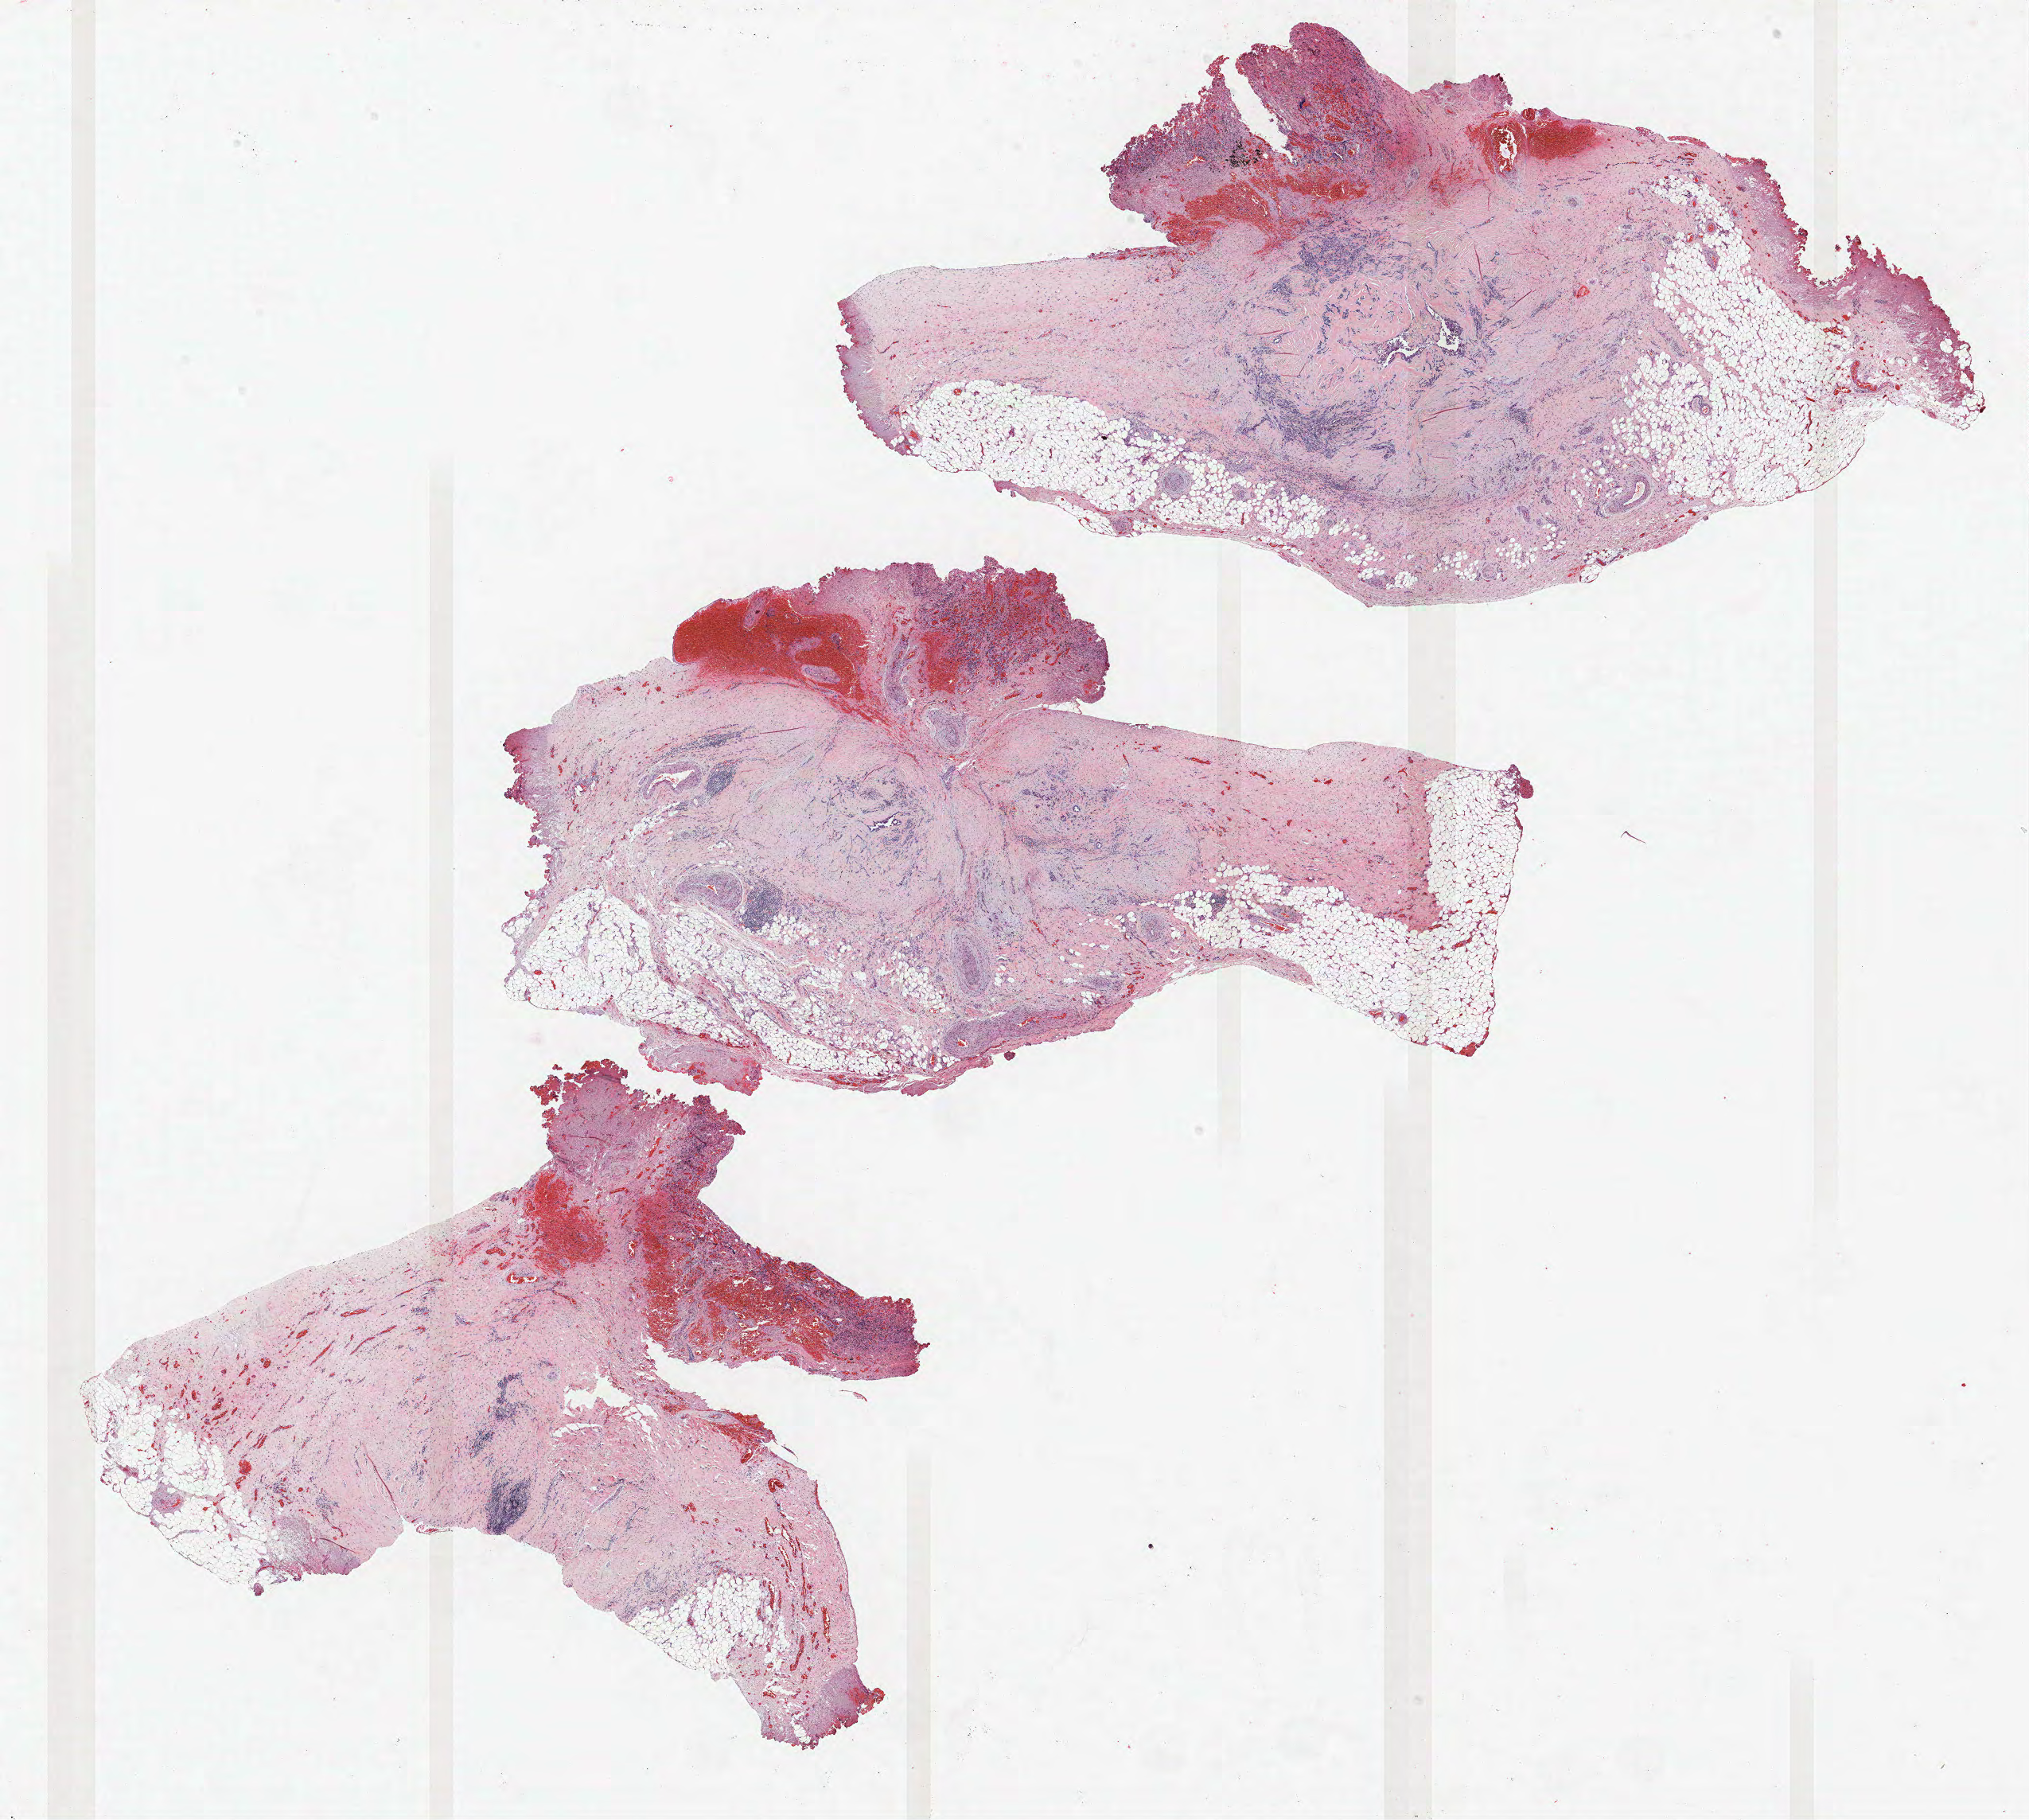
H&E-stained whole-slide image — low-resolution overview of the scanned area, about 20.4 x 18.3 mm (slide scanned at 40x); formalin-fixed paraffin-embedded (FFPE) section; lung. Male patient, aged 62 at enrolment. Former smoker at enrolment.
Participant's lung-cancer diagnosis: Adenocarcinoma, NOS (ICD-O-3 8140/3).